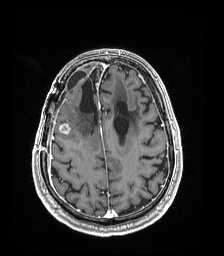
Brain MRI from a brain-tumour surgery series, one axial slice; slice 55 of 192 in the series (ordered by position); T1-weighted post-contrast; 1 mm slice thickness; 224 × 256 image matrix, field of view 224 × 256 mm. From the clinical record (not read from this slice): histopathology: Astrocytoma; WHO grade: 4; IDH mutation: yes.
Outlined on this slice (manually delineated by an expert):
- previous resection cavity: bounding box [x1, y1, x2, y2] px = [80, 69, 98, 123]